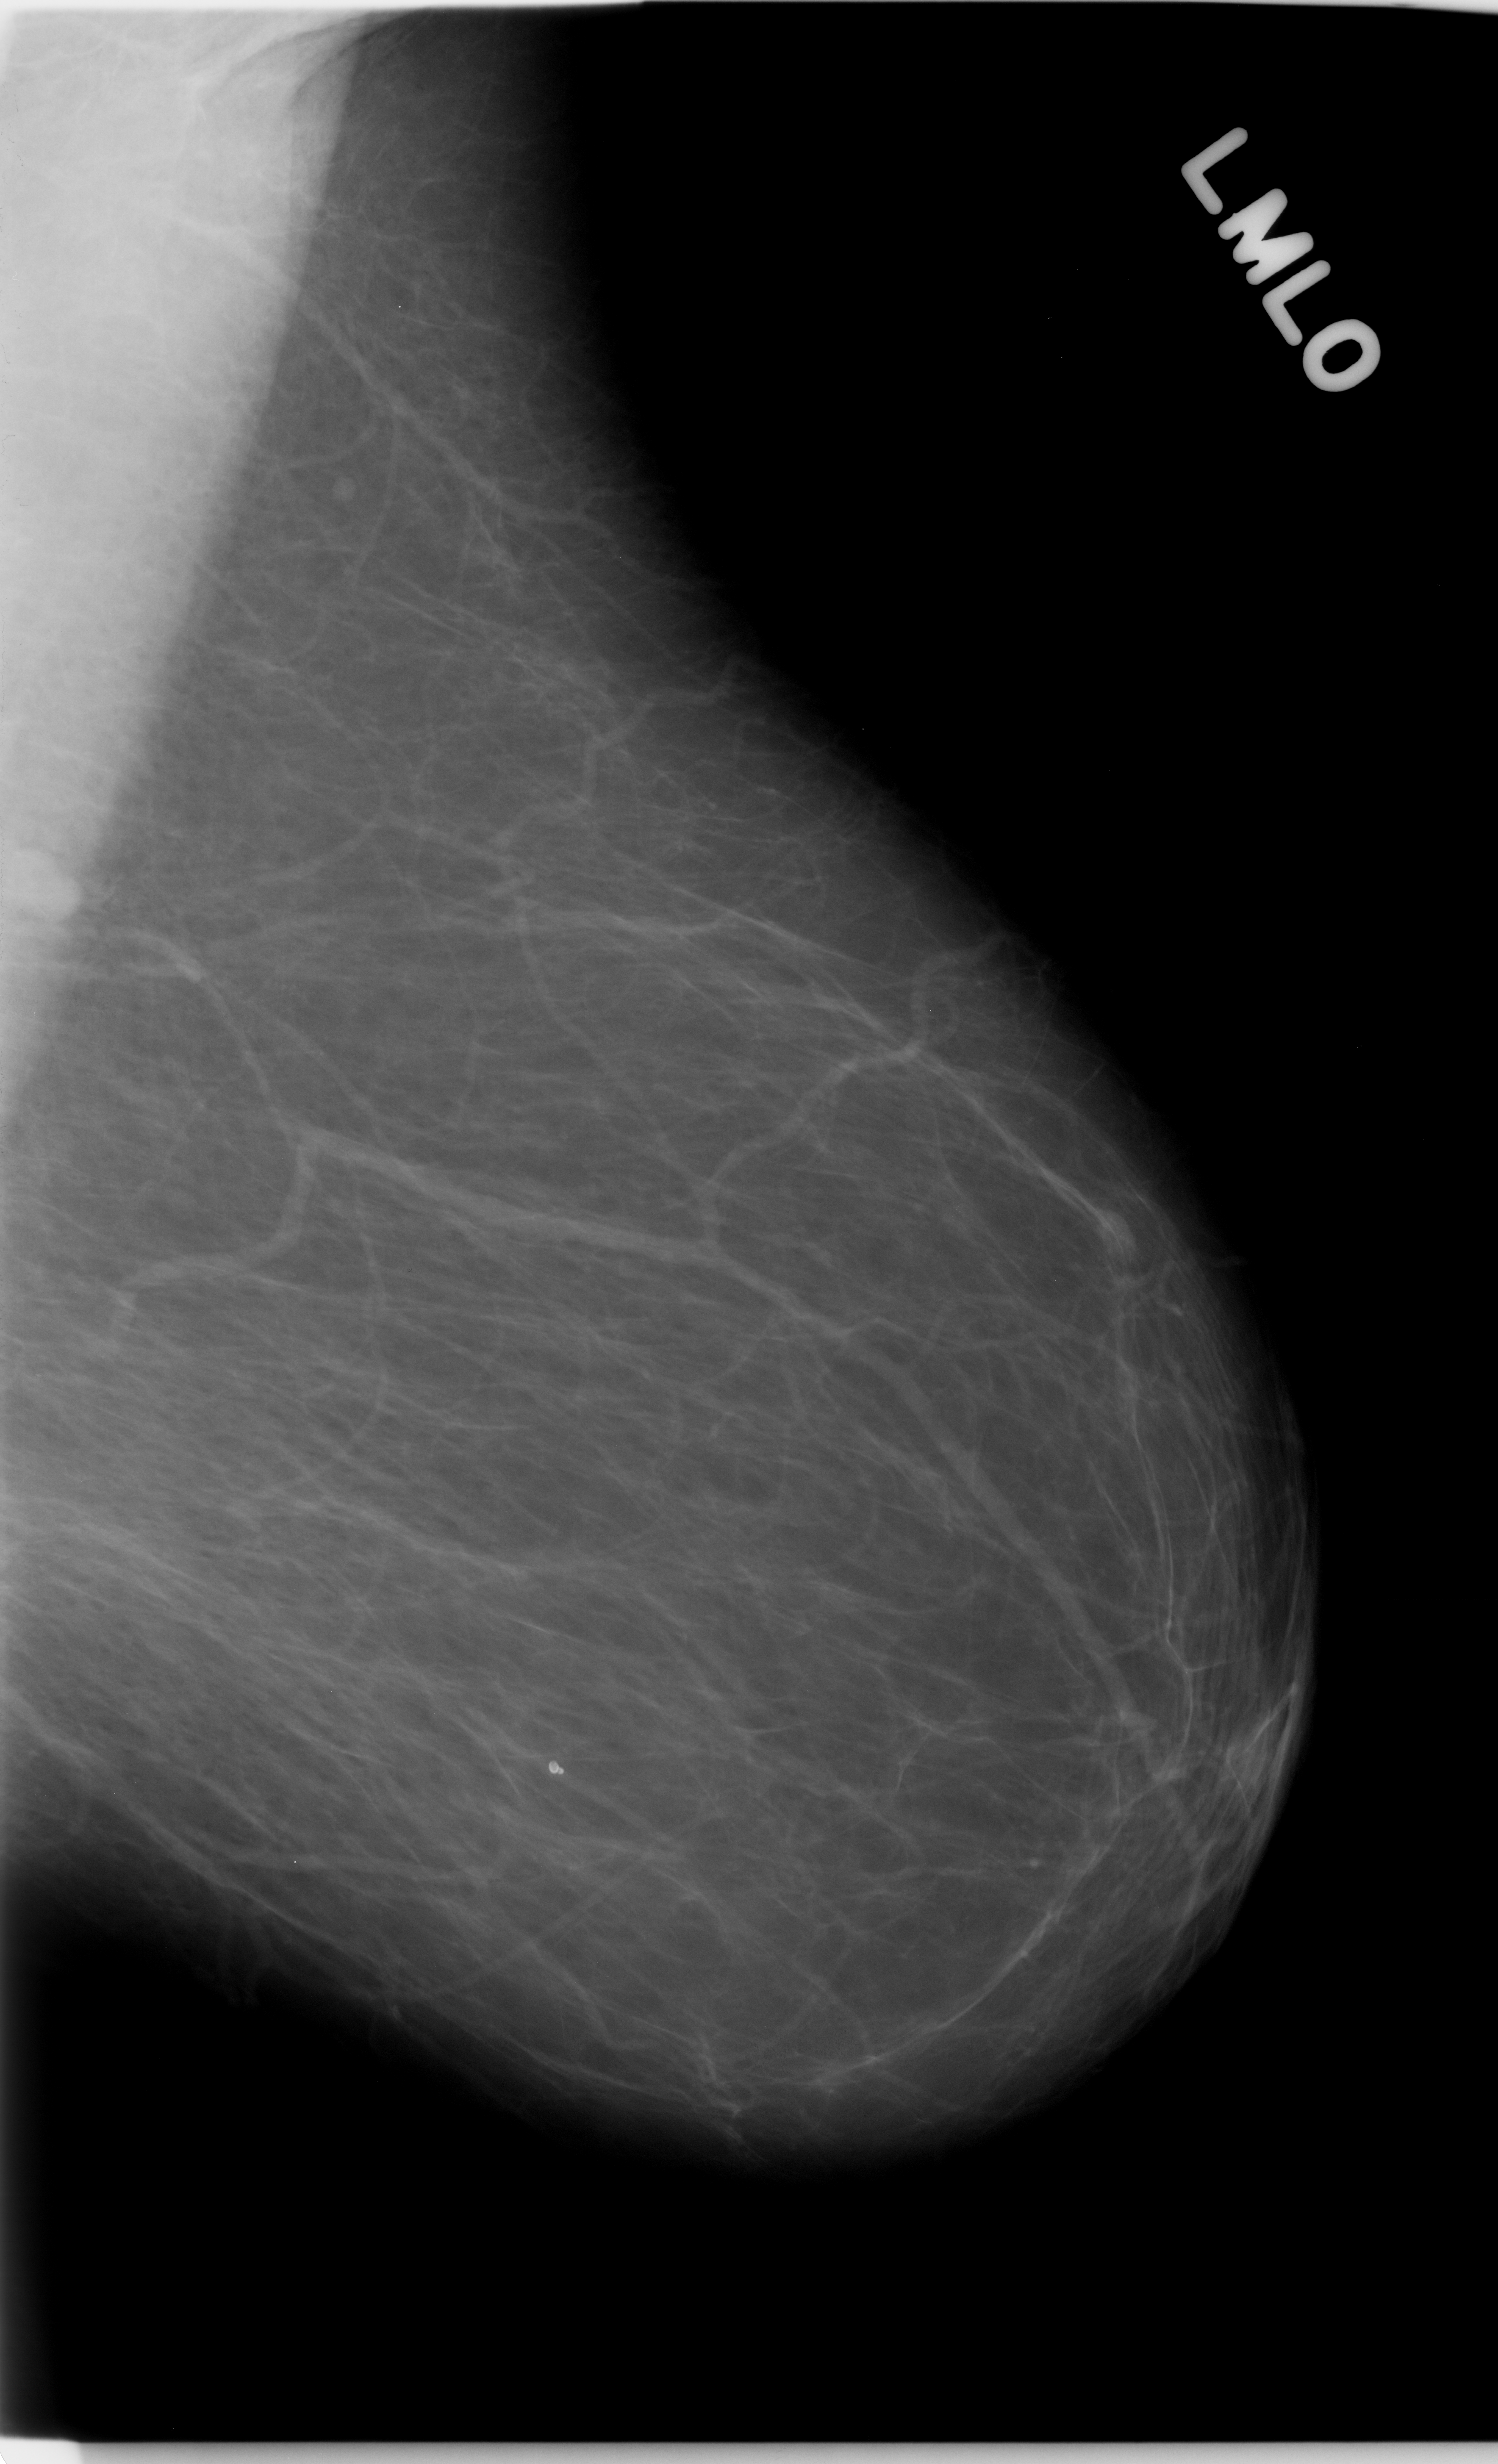
Digitized screen-film mammogram. Left breast. Mediolateral oblique (MLO) view. Breast composition: almost entirely fatty (BI-RADS density category 1 of 4). 1498 × 2464 image matrix.
Marked abnormalities (boxes around the expert regions of interest):
- mass, shape oval, margins circumscribed; BI-RADS assessment category 4; pathology (as recorded): malignant: box from (x=1067, y=1187) to (x=1141, y=1294) px